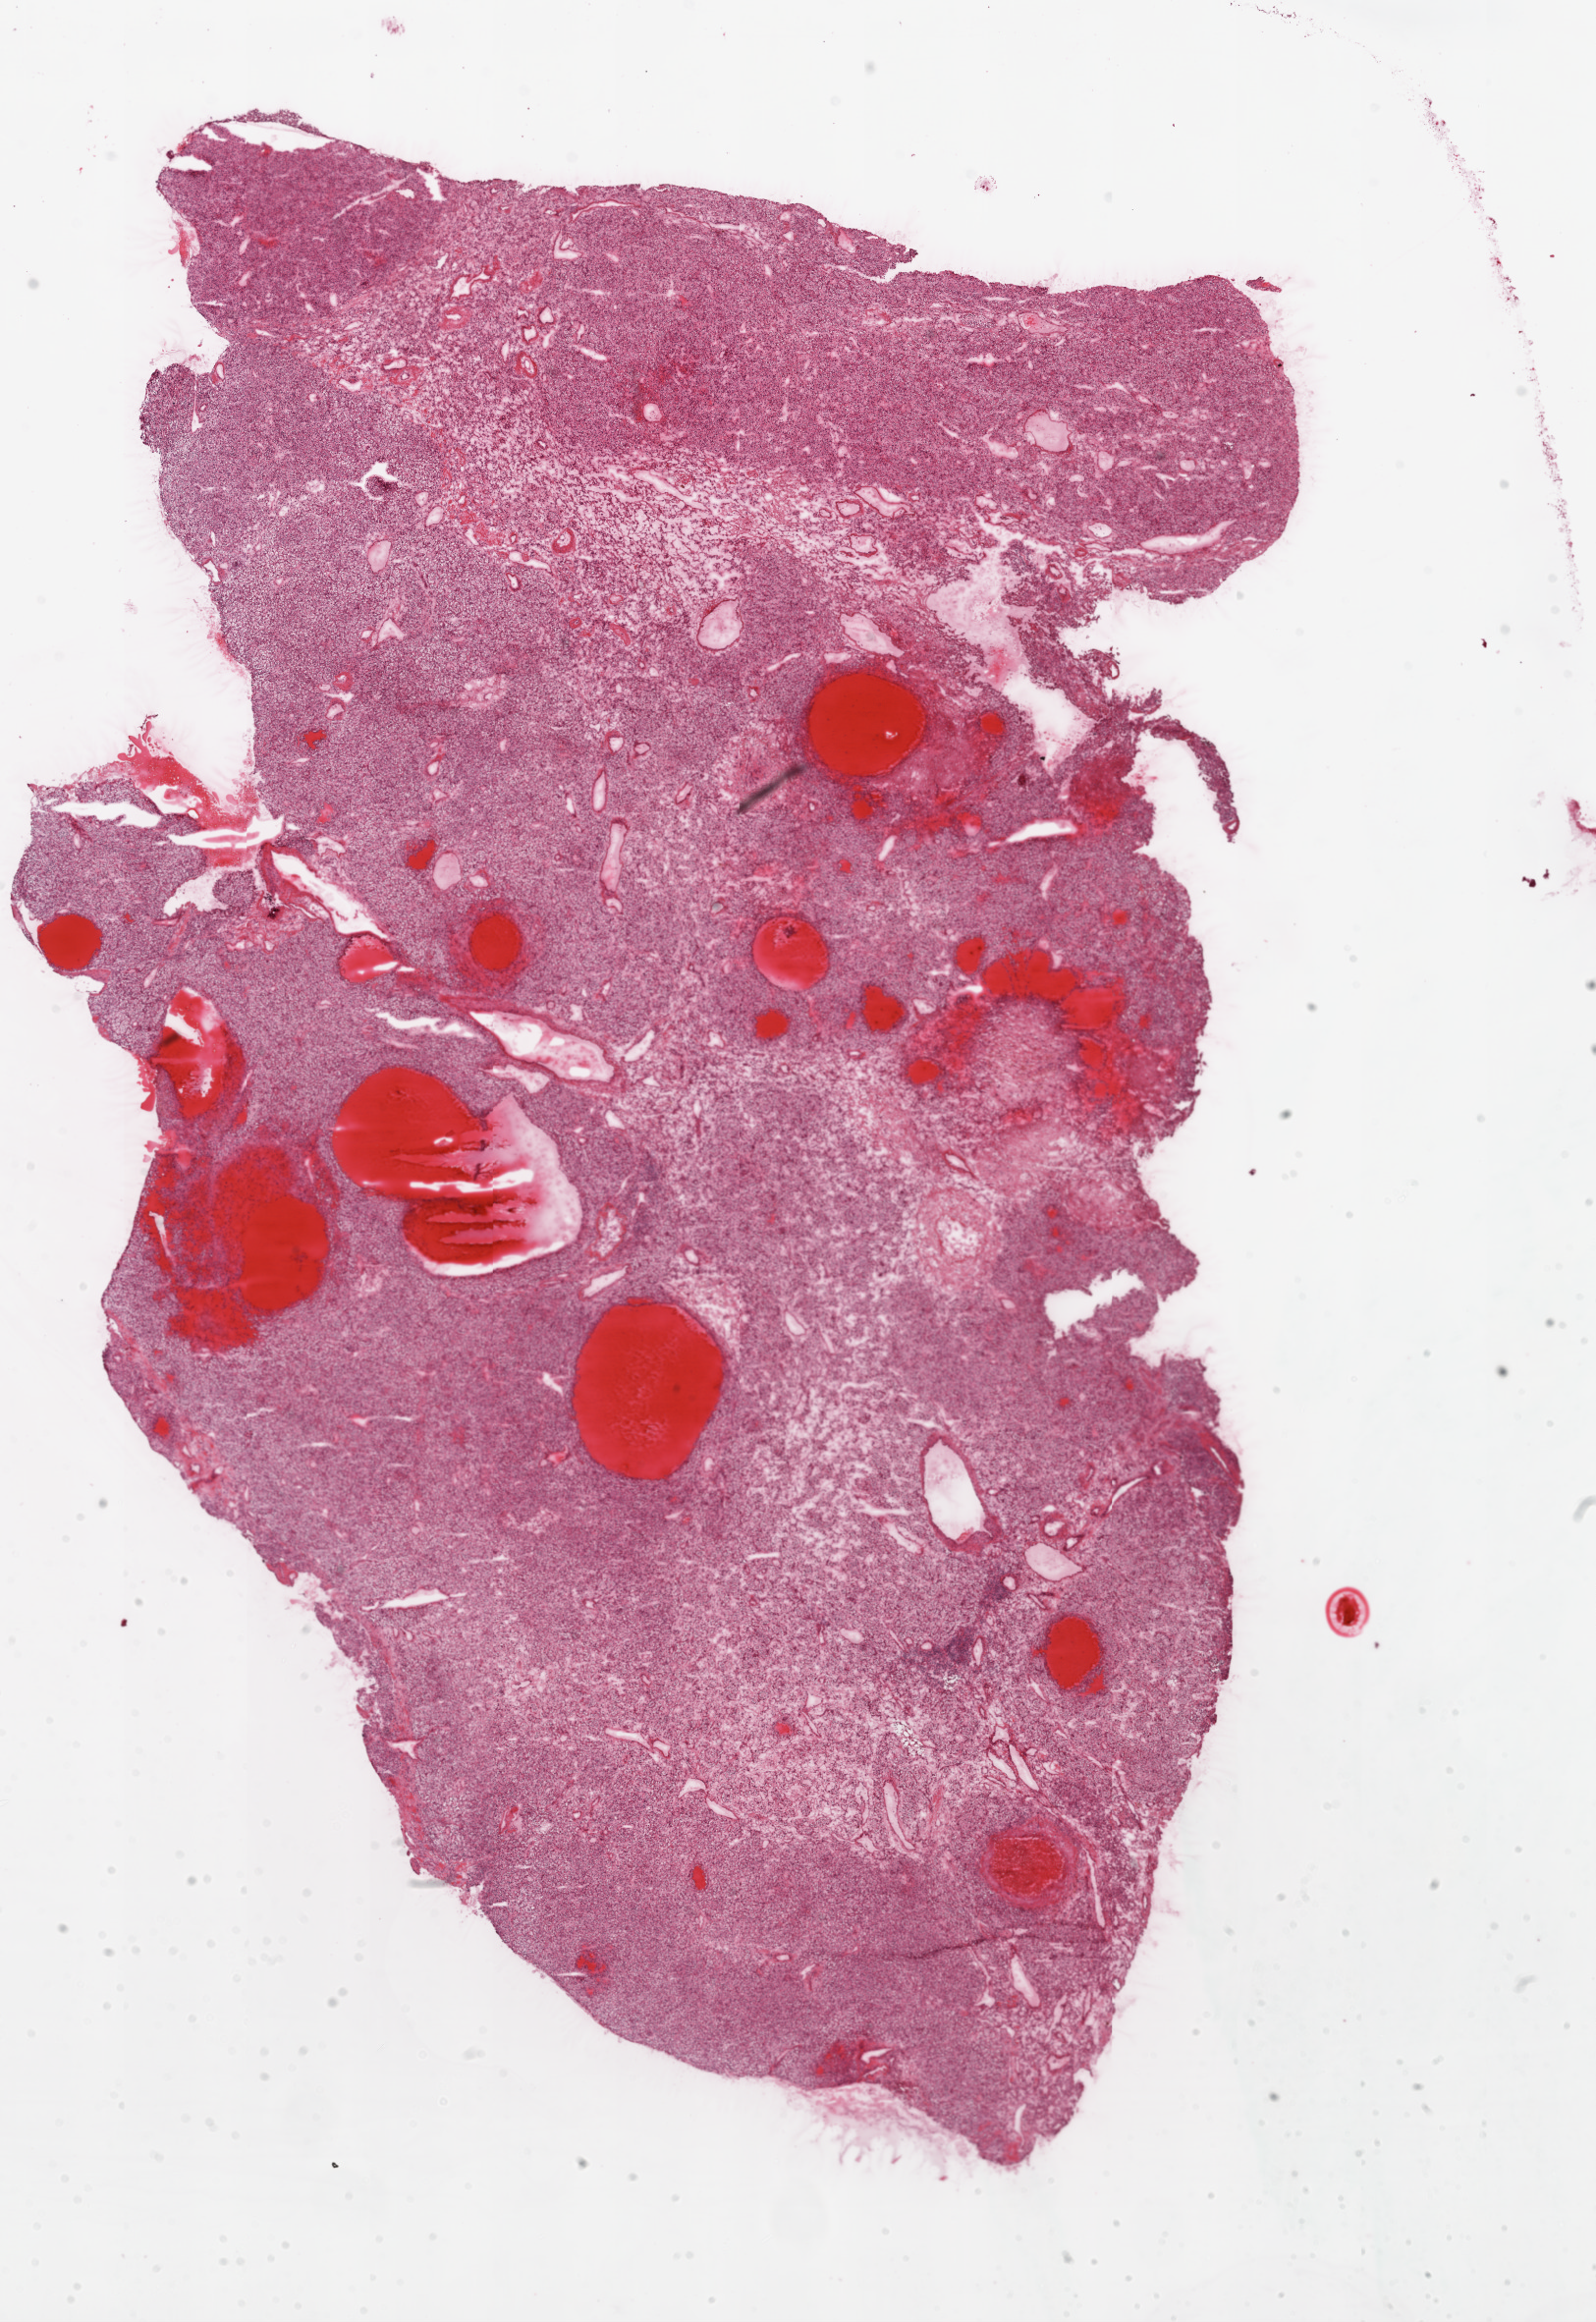
Whole-slide histology image, Hematoxylin and eosin (H&E) stained, a low-resolution overview of the entire scanned area, about 13.0 x 19.0 mm, frozen section from the top of the tissue portion, kidney, primary tumour sample. Male patient; age at initial diagnosis 47 years. Histologic grade: G2 (moderately differentiated). Pathologist review of this section (percent, as recorded): tumour cells 85%, tumour nuclei 85%, normal cells 0%, stromal cells 15%, necrosis 0%.
Histologic diagnosis: Clear cell adenocarcinoma, NOS. AJCC pathologic stage: I.